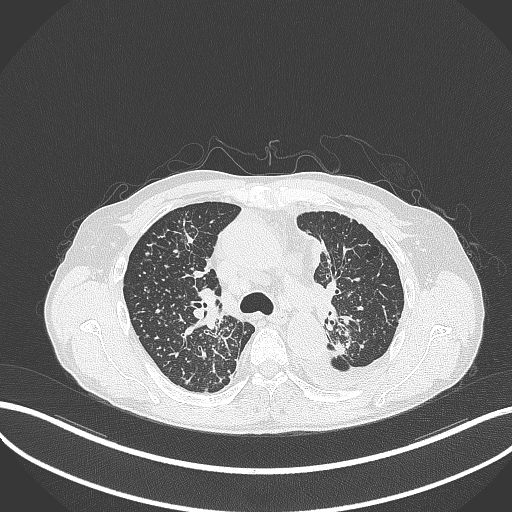
Chest CT, one axial slice; position 245 of 325 along the scan axis; lung window (W 1500 / L -600 HU); 1 mm slice thickness; 512 × 512 image matrix. Male patient, age 58 years. From the clinical record (not read from this slice): clinical TNM (as recorded): T1c N3 M1.
Annotated regions visible in this slice (bounding box drawn by a radiologist):
- lung tumour (recorded histology: adenocarcinoma): bounding box [x1, y1, x2, y2] px = [333, 339, 346, 358]